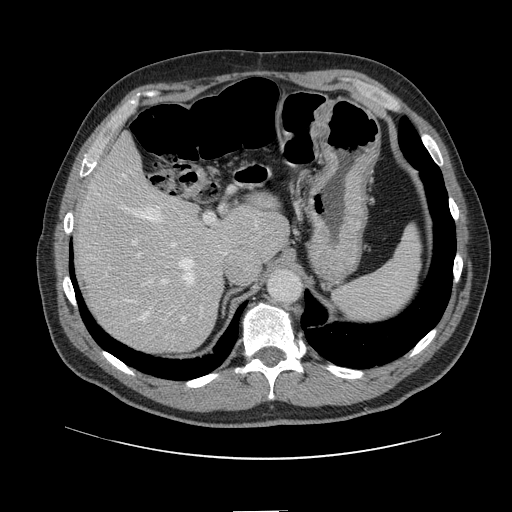
Contrast-enhanced abdominal CT, one axial slice. Position 97 of 161 along the scan axis. Intravenous contrast given. Soft-tissue window (W 400 / L 40 HU). 512 × 512 image matrix, field of view 412 × 412 mm. Male patient, age 66 years. Case-level facts recorded for this patient, not image findings: diagnosis: colorectal cancer liver metastases, imaged before liver resection.
Annotated regions visible in this slice (outlined manually by an expert reader):
- hepatic veins: bounding box [x1, y1, x2, y2] px = [120, 175, 194, 320]
- liver: [80, 141, 286, 352]
- planned liver remnant (the part of the liver to remain after resection): [81, 140, 286, 305]
- portal vein (with intrahepatic branches): [131, 212, 216, 314]